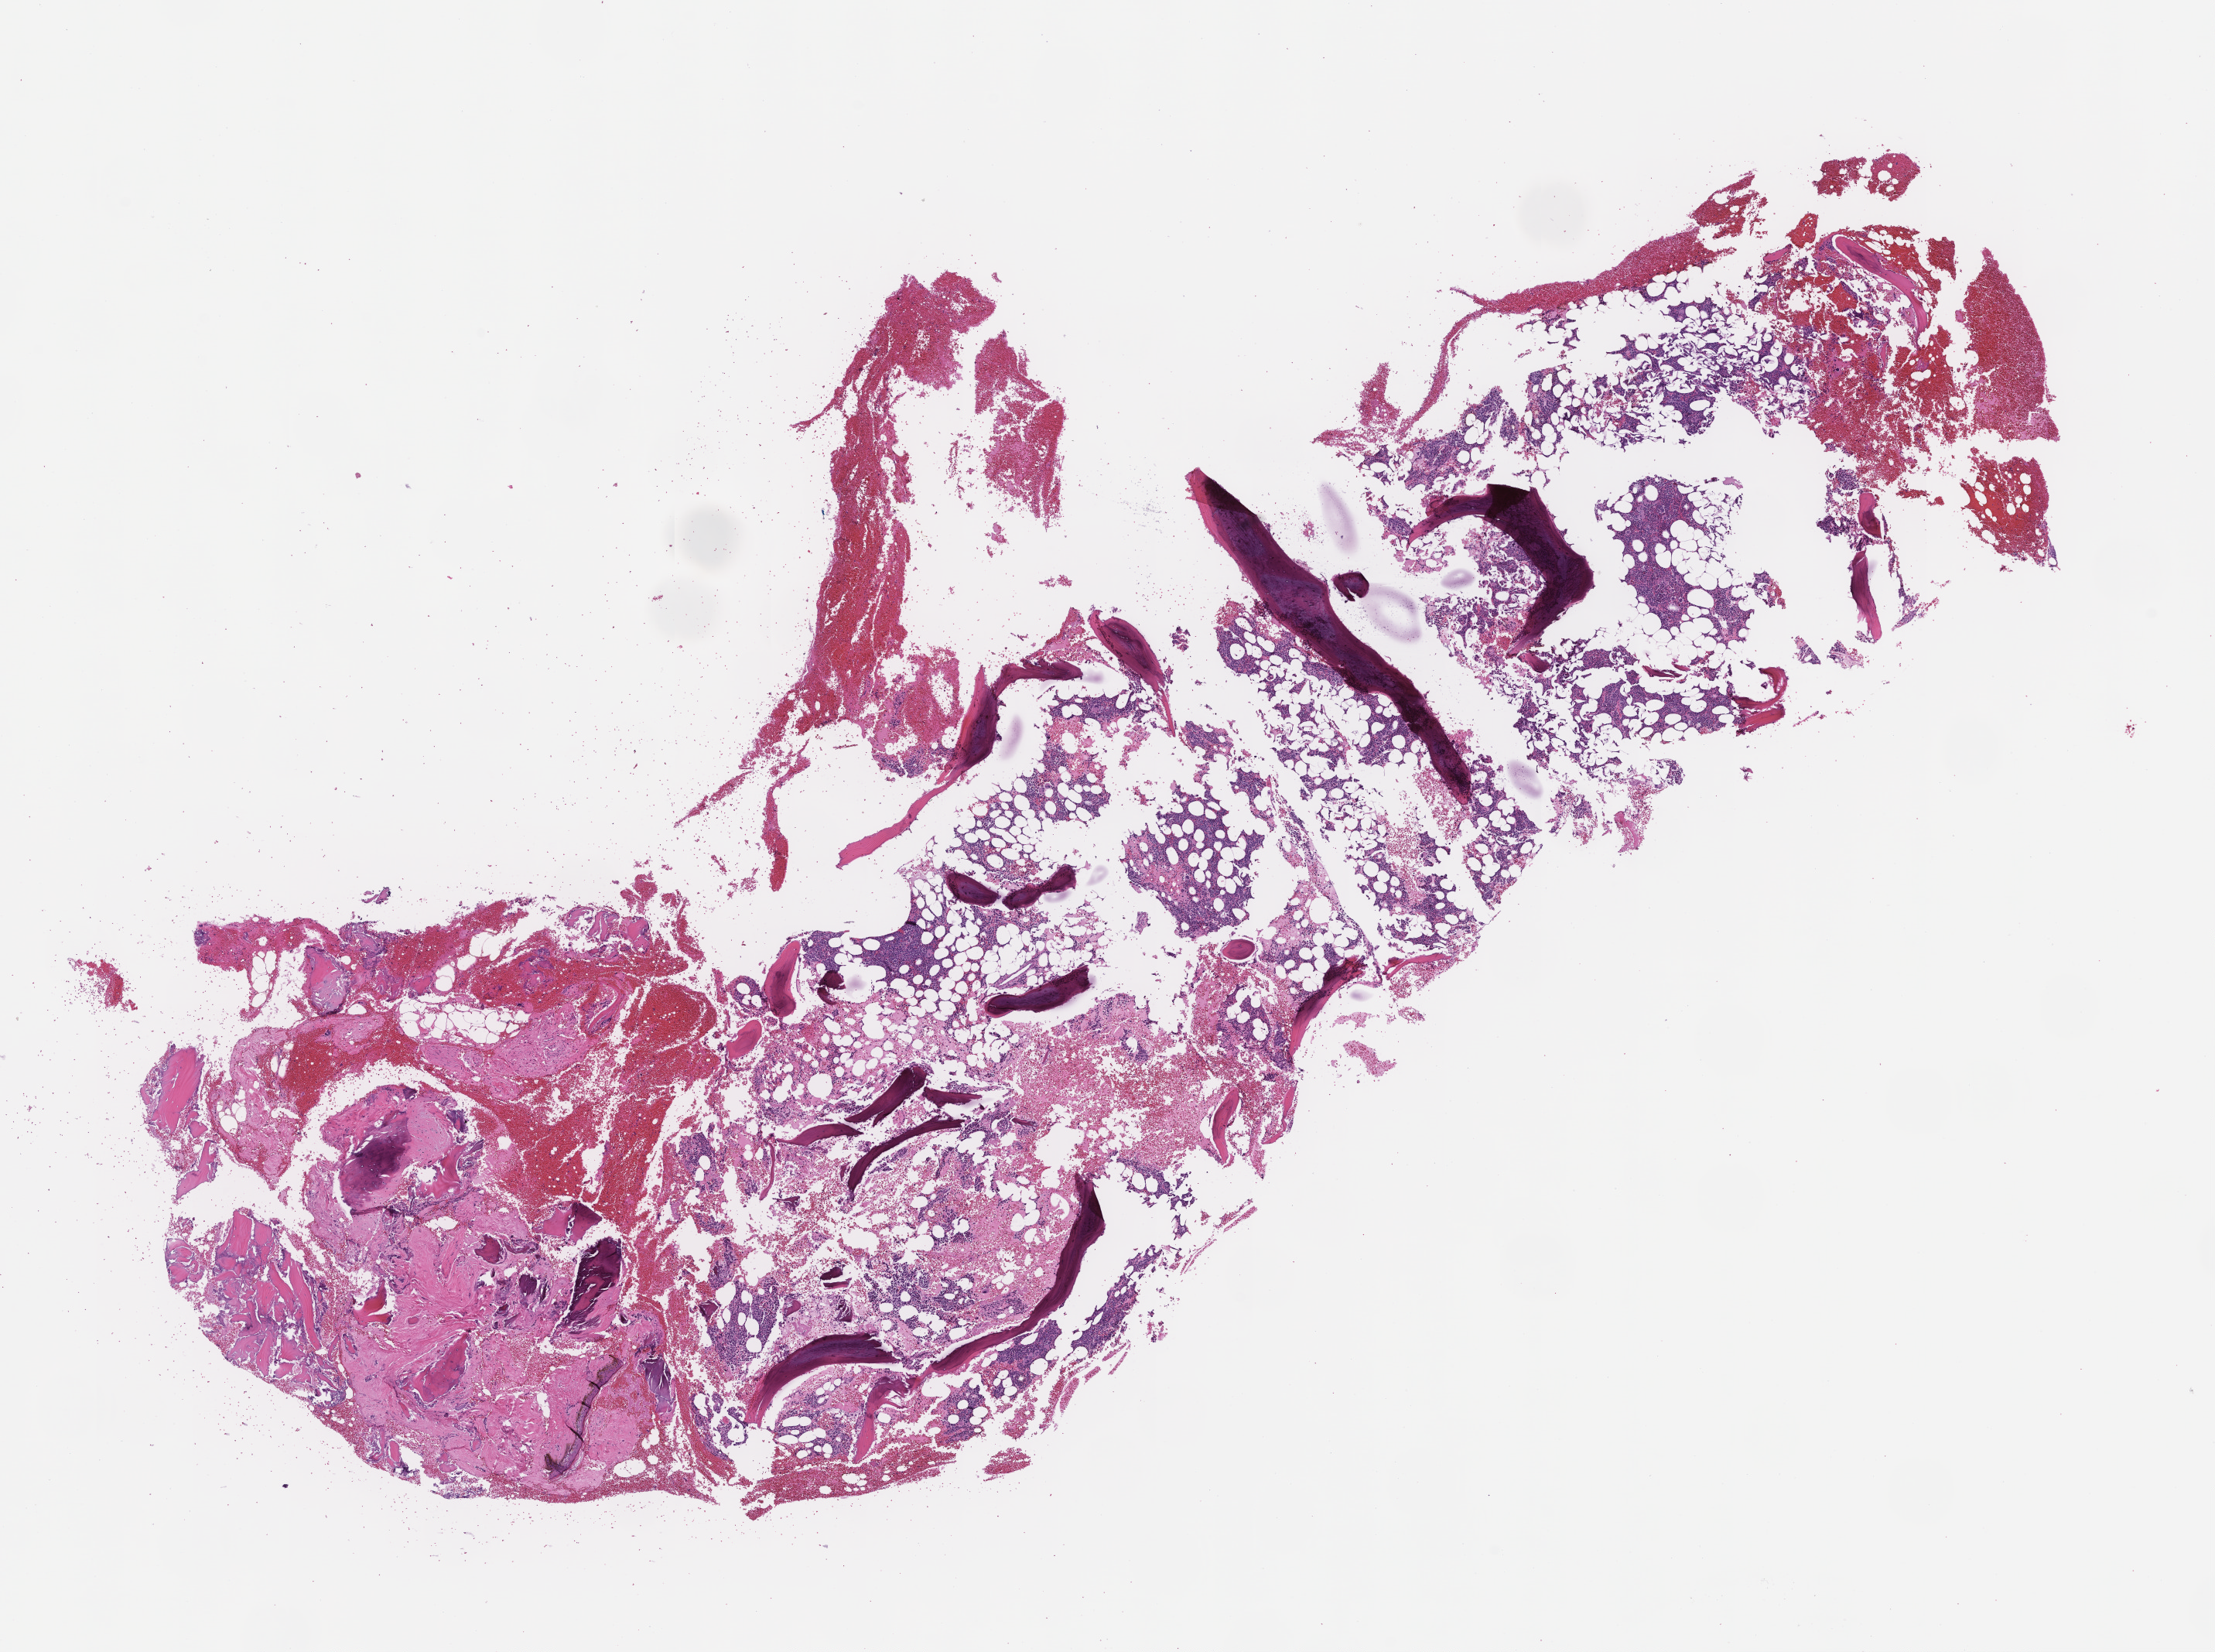
Whole-slide image, hematoxylin and eosin (H&E) stain, a low-resolution overview of the entire scanned area, about 11.6 x 8.6 mm, formalin-fixed, paraffin-embedded (FFPE) tissue, tissue site: bone marrow, specimen time point: archival tissue. Patient sex: female.
* this section: primary tumor
* diagnosis: Plasma Cell Myeloma